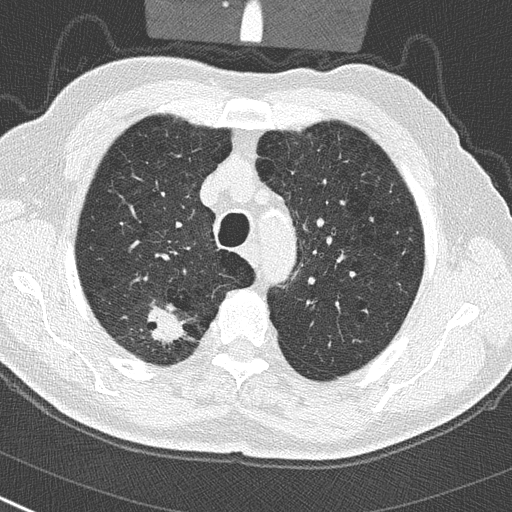
Low-dose screening chest CT, one axial slice; slice 225 of 290 in the series (ordered by position); 120 kVp; lung window (W 1500 / L -600 HU); 2 mm slice thickness; 512 × 512 image matrix.
Annotated regions visible in this slice (expert manual segmentation):
- lesion 1 (tumor, upper lobe of right lung): box from (x=142, y=307) to (x=186, y=349) px